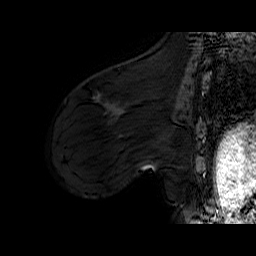
Breast MRI (dynamic contrast-enhanced), one sagittal slice; slice 23 of 60 in the series (ordered by position); dynamic contrast-enhanced series, time point 2 of 6 at this slice position (early post-contrast); 1.5 T; TE 6.4 ms, TR 32.9 ms; 4 mm slice thickness; 256 × 256 image matrix, field of view 200 × 200 mm. Female patient. Case-level facts recorded for this patient, not image findings: setting: breast cancer imaged before/during neoadjuvant chemotherapy; receptor status: HER2-positive.
Structures marked on this image (semi-automatically segmented with operator editing):
- analysis volume of interest (the breast-tissue region the enhancement analysis was run in; not a lesion): bounding box <78,94,152,149> (left, top, right, bottom; pixels)
- tumour enhancement mask (voxels above the 100 % enhancement threshold inside the analysis volume of interest): <93,96,100,99>